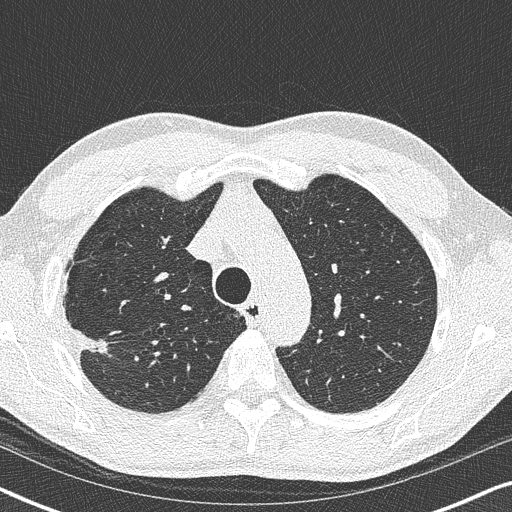
Low-dose screening chest CT, one axial slice. Slice 279 of 356 in the series (ordered by position). Reconstruction kernel B50f. Lung window (W 1500 / L -600 HU). 1 mm slice thickness. 512 × 512 image matrix, field of view 330 × 330 mm.
Annotated regions visible in this slice (outlined manually by an expert reader):
- lesion 1 (tumor, upper lobe of right lung): bounding box [x1, y1, x2, y2] px = [74, 327, 107, 353]